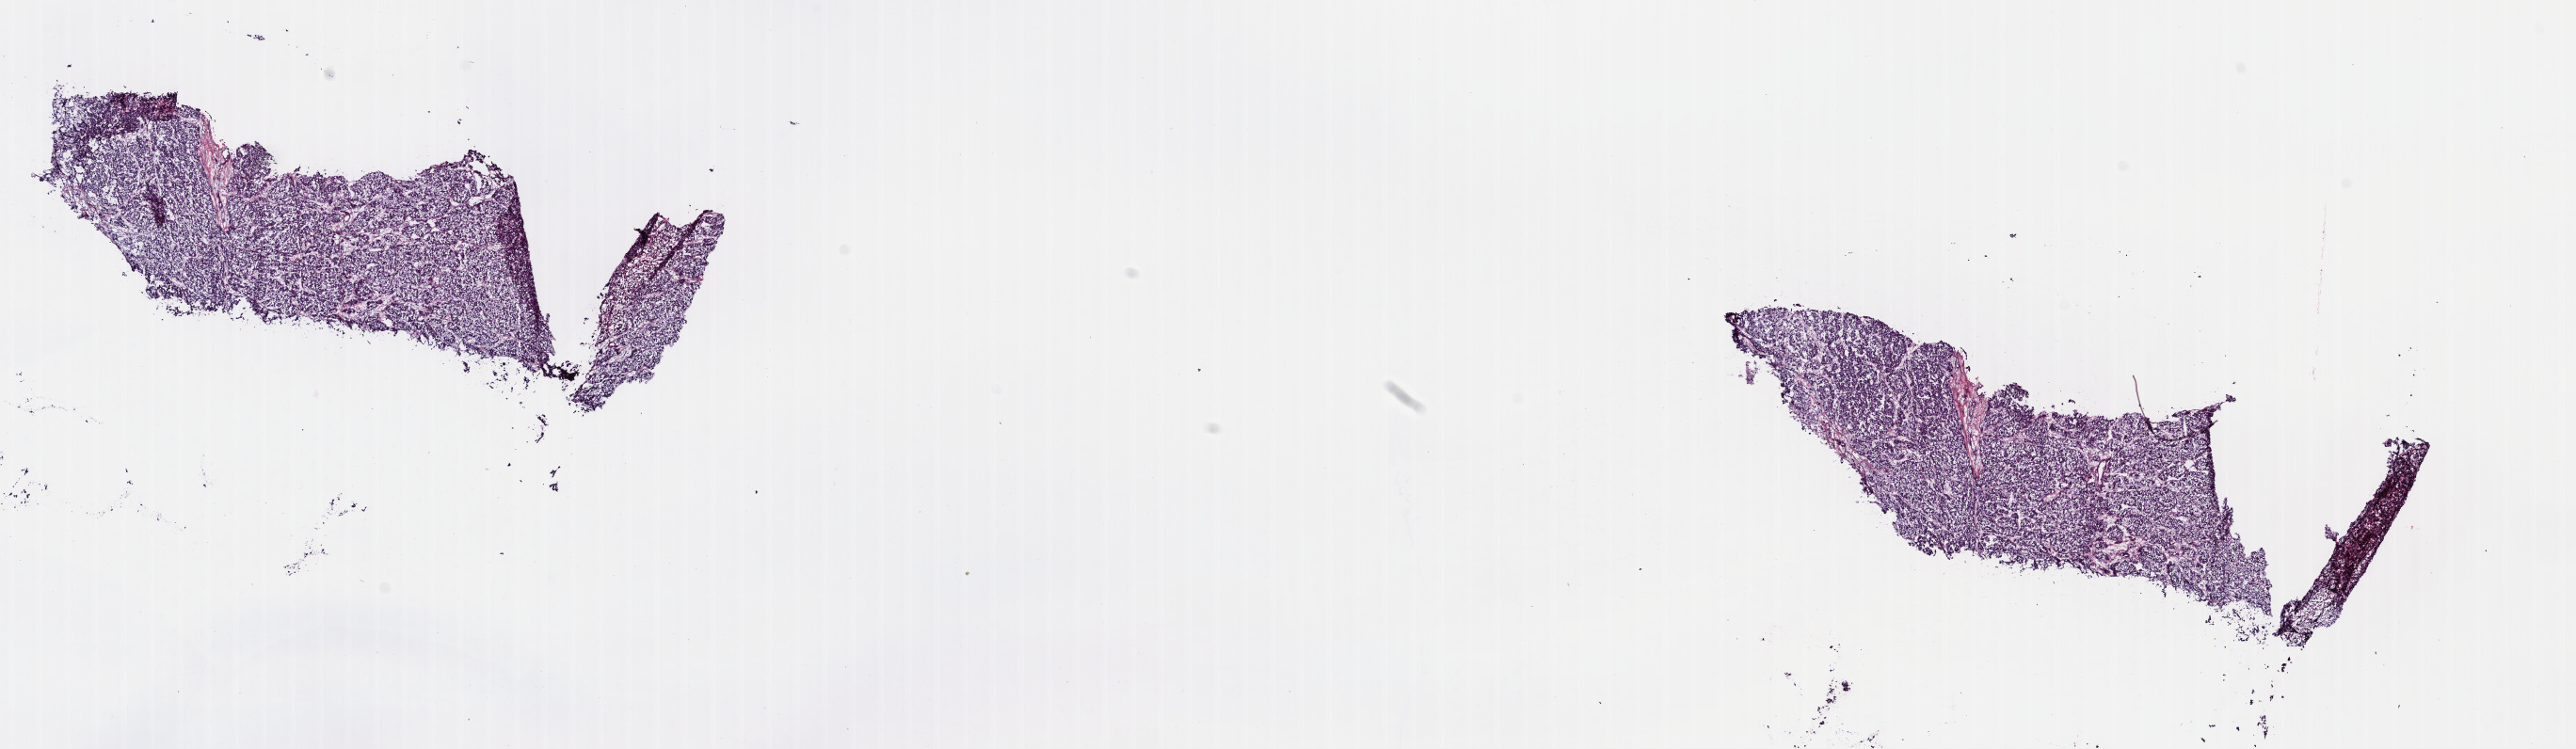
H&E whole-slide image, shown as a low-resolution overview of the whole scanned area (about 21.5 x 6.3 mm, acquisition: 40x scan), frozen section from the top of the tissue portion, primary tumour sample from the liver. Female, age 75 years at initial diagnosis. Histologic grade: G3 (poorly differentiated). Slide review estimates, as recorded: tumour cells 100%, tumour nuclei 80%, normal cells 0%, stromal cells 0%, necrosis 0%. Inflammatory infiltration, as recorded: lymphocyte infiltration 2%, monocyte infiltration 0%, neutrophil infiltration 0%.
TNM: T3a N0 M0. AJCC pathologic stage: IIIA (7th edition). Diagnosis: Hepatocellular carcinoma, NOS.